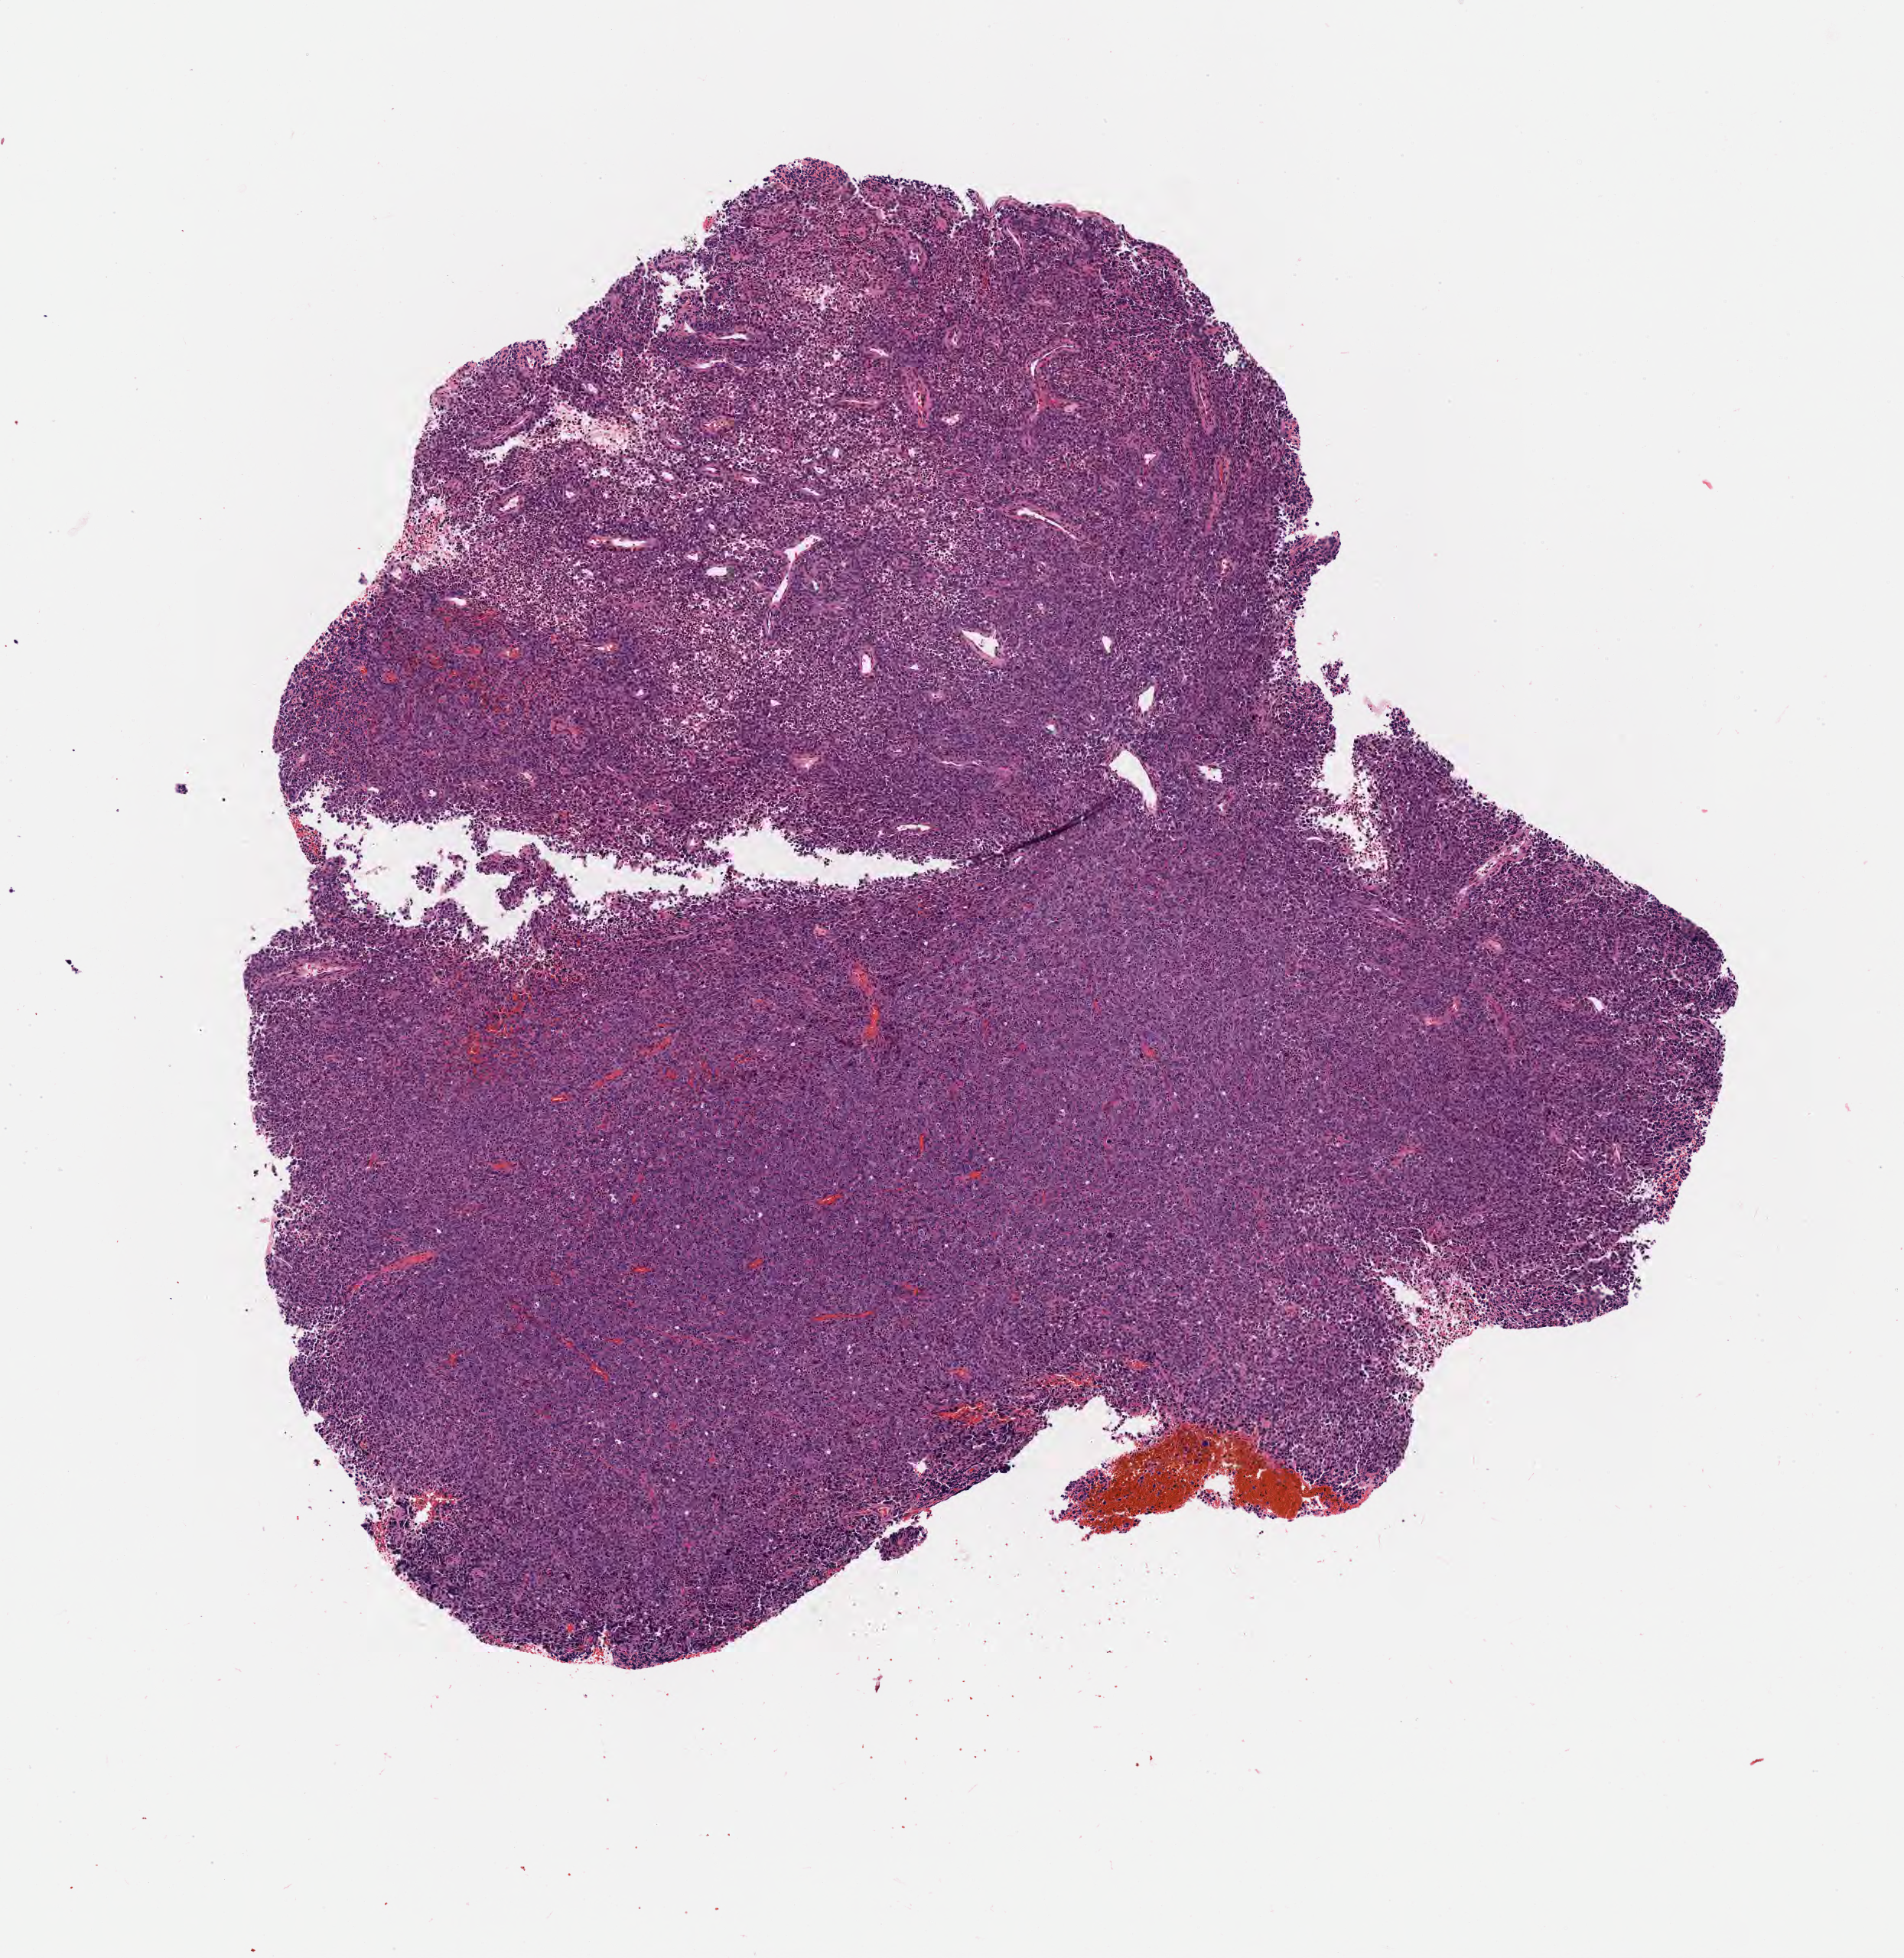
Digitized H&E-stained section — a low-resolution overview of the entire scanned area, about 5.0 x 5.2 mm; tumor tissue; site: cervix. Patient: female, age 70 years.
Diagnosis: Squamous cell carcinoma, large cell, nonkeratinizing, NOS.